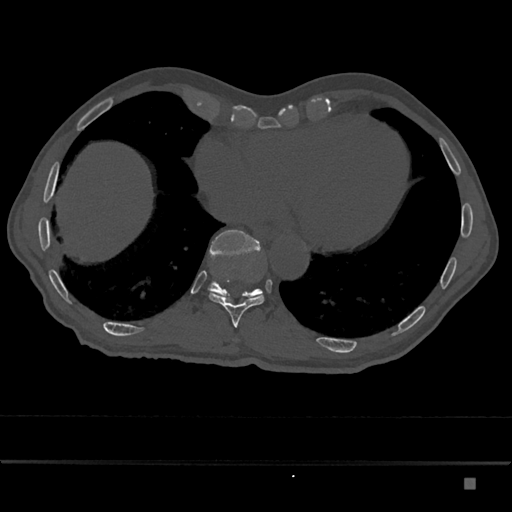
CT including the spine, one axial slice; reconstruction kernel Br40s/3; 120 kVp; bone window (W 1800 / L 400 HU); 0.5 mm slice thickness; 512 × 512 image matrix, field of view 390 × 390 mm. Patient: male, 72 years. From the clinical record (not read from this slice): primary cancer: prostate.
Outlined on this slice (semi-automatically segmented with operator editing):
- T10 vertebra: box from (x=209, y=293) to (x=265, y=328) px
- T11 vertebra: (x=208, y=230)–(x=263, y=301)